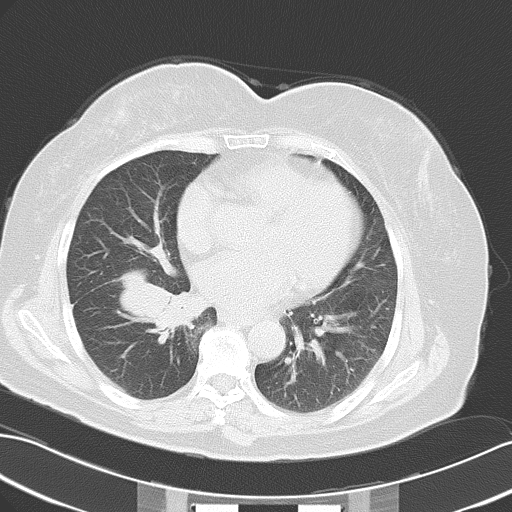
Chest CT, one axial slice. Position 24 of 50 along the scan axis. Reconstruction kernel B70f. 120 kVp. Lung window (W 1500 / L -600 HU). 5 mm slice thickness. 512 × 512 image matrix, field of view 353 × 353 mm. Patient: female, 63 years. From the clinical record (not read from this slice): clinical TNM (as recorded): T3 N0 M0.
Outlined on this slice (rectangle marked by the reading radiologist):
- lung tumour (recorded histology: adenocarcinoma): box from (x=108, y=268) to (x=201, y=343) px